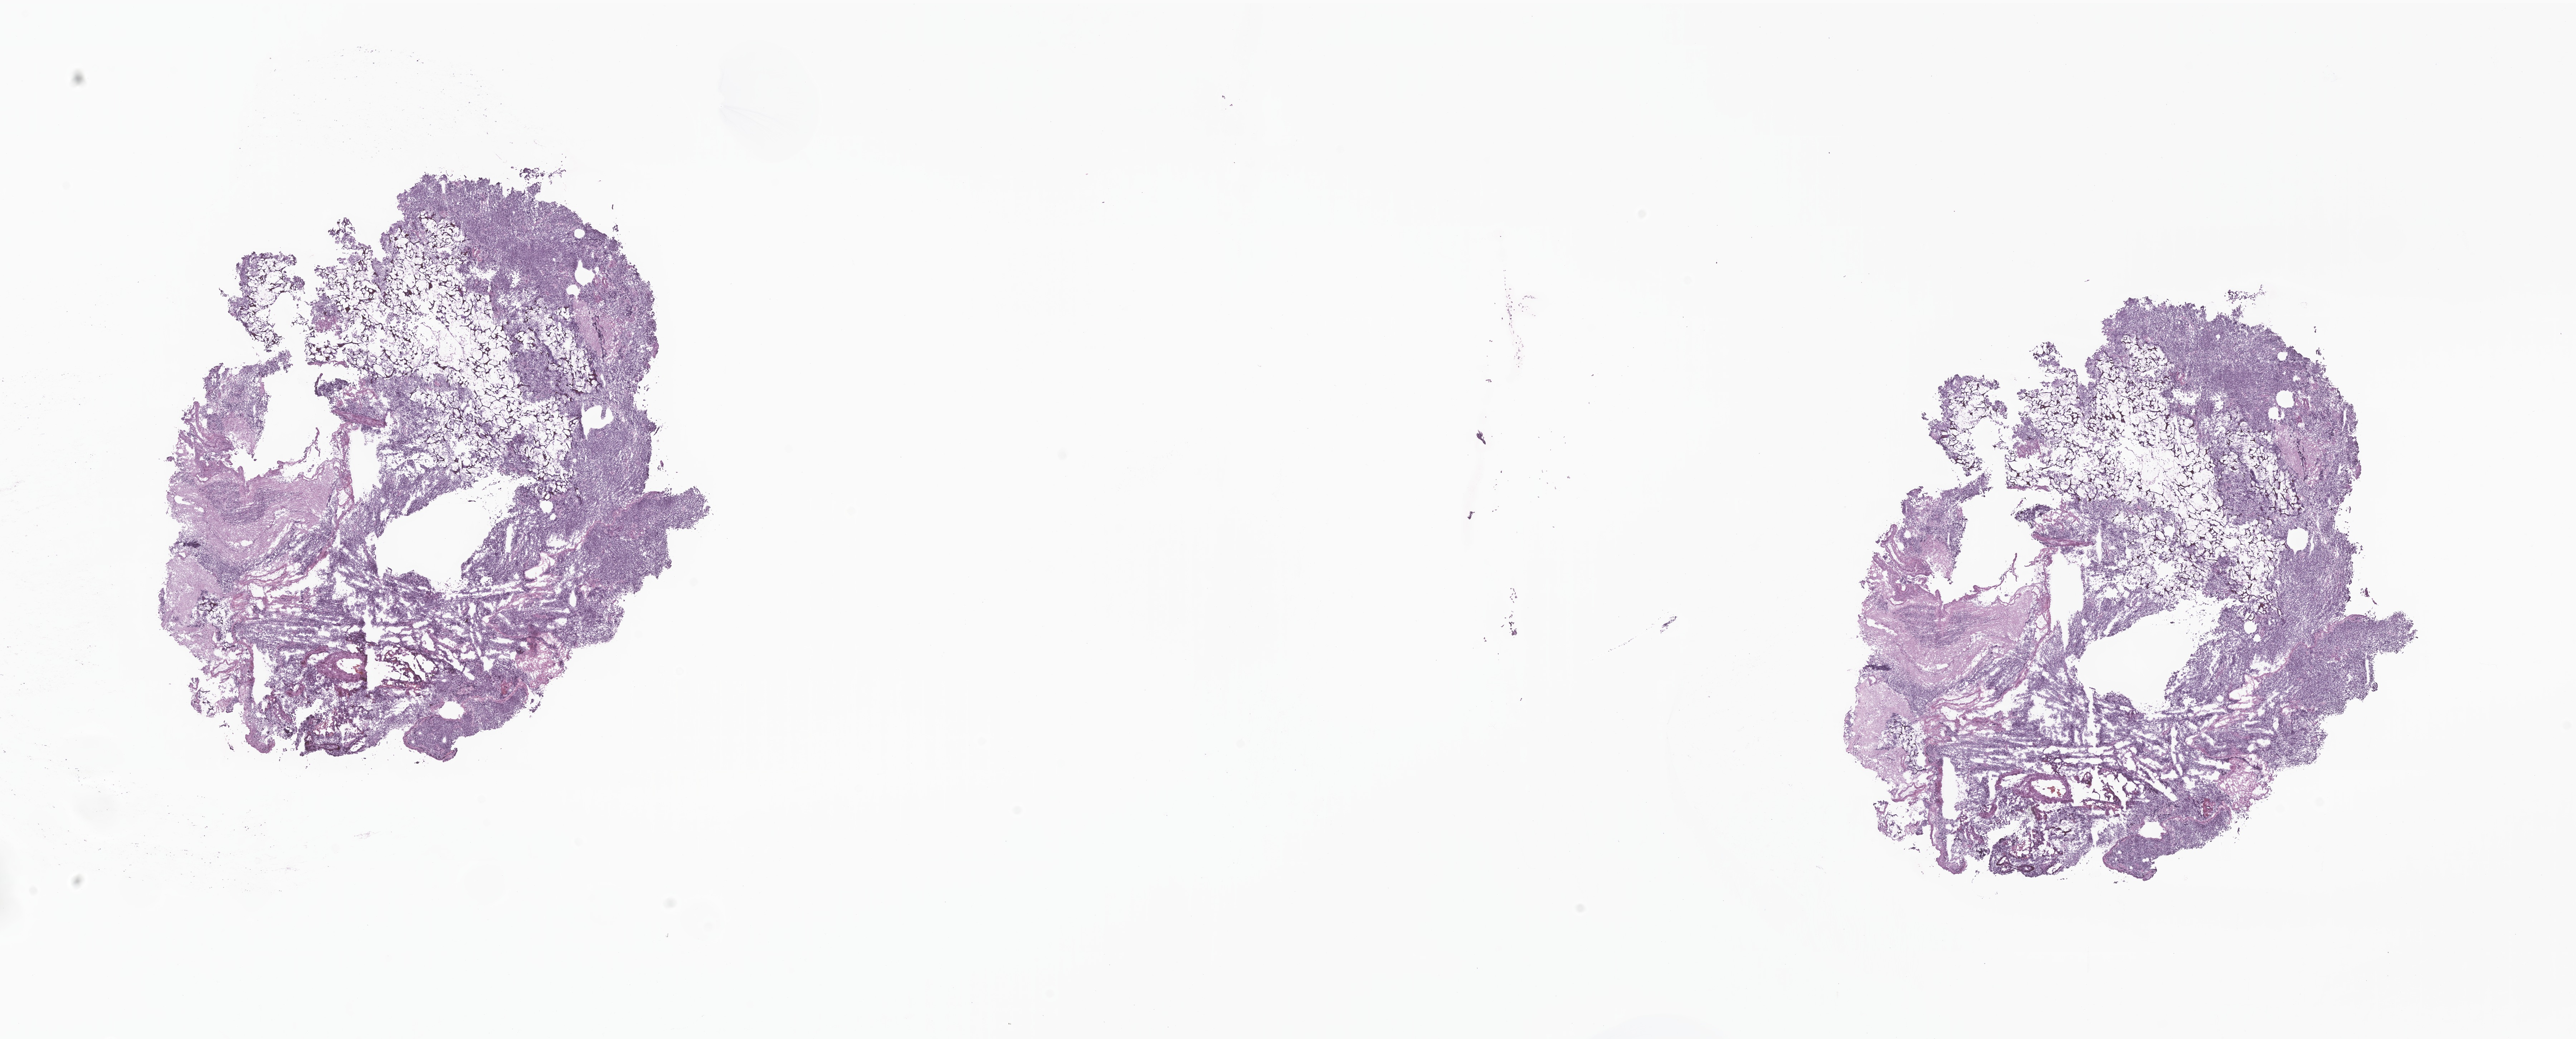
H&E whole-slide image of tumor tissue from the cerebellum, a low-resolution overview of the entire scanned area, about 30.3 x 12.2 mm, cryosection (OCT / tissue freezing medium). Patient: male, age 74 months (6 years 2 months).
Recorded diagnosis: Medulloblastoma, NOS.